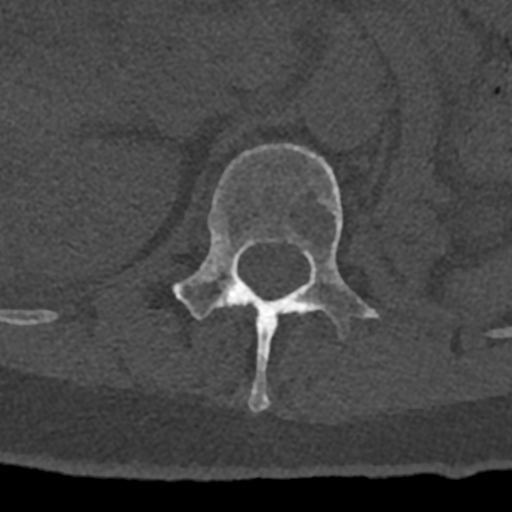
CT including the spine, one axial slice. Position 442 of 797 along the scan axis. 120 kVp. Bone window (W 1800 / L 400 HU). 0.5 mm slice thickness. 512 × 512 image matrix. Patient: male, 74 years. From the clinical record (not read from this slice): primary cancer: renal.
Structures marked on this image (semi-automatically segmented with operator editing):
- L1 vertebra: bounding box <173,143,380,412> (left, top, right, bottom; pixels)
- T12 vertebra: <225,302,245,307>